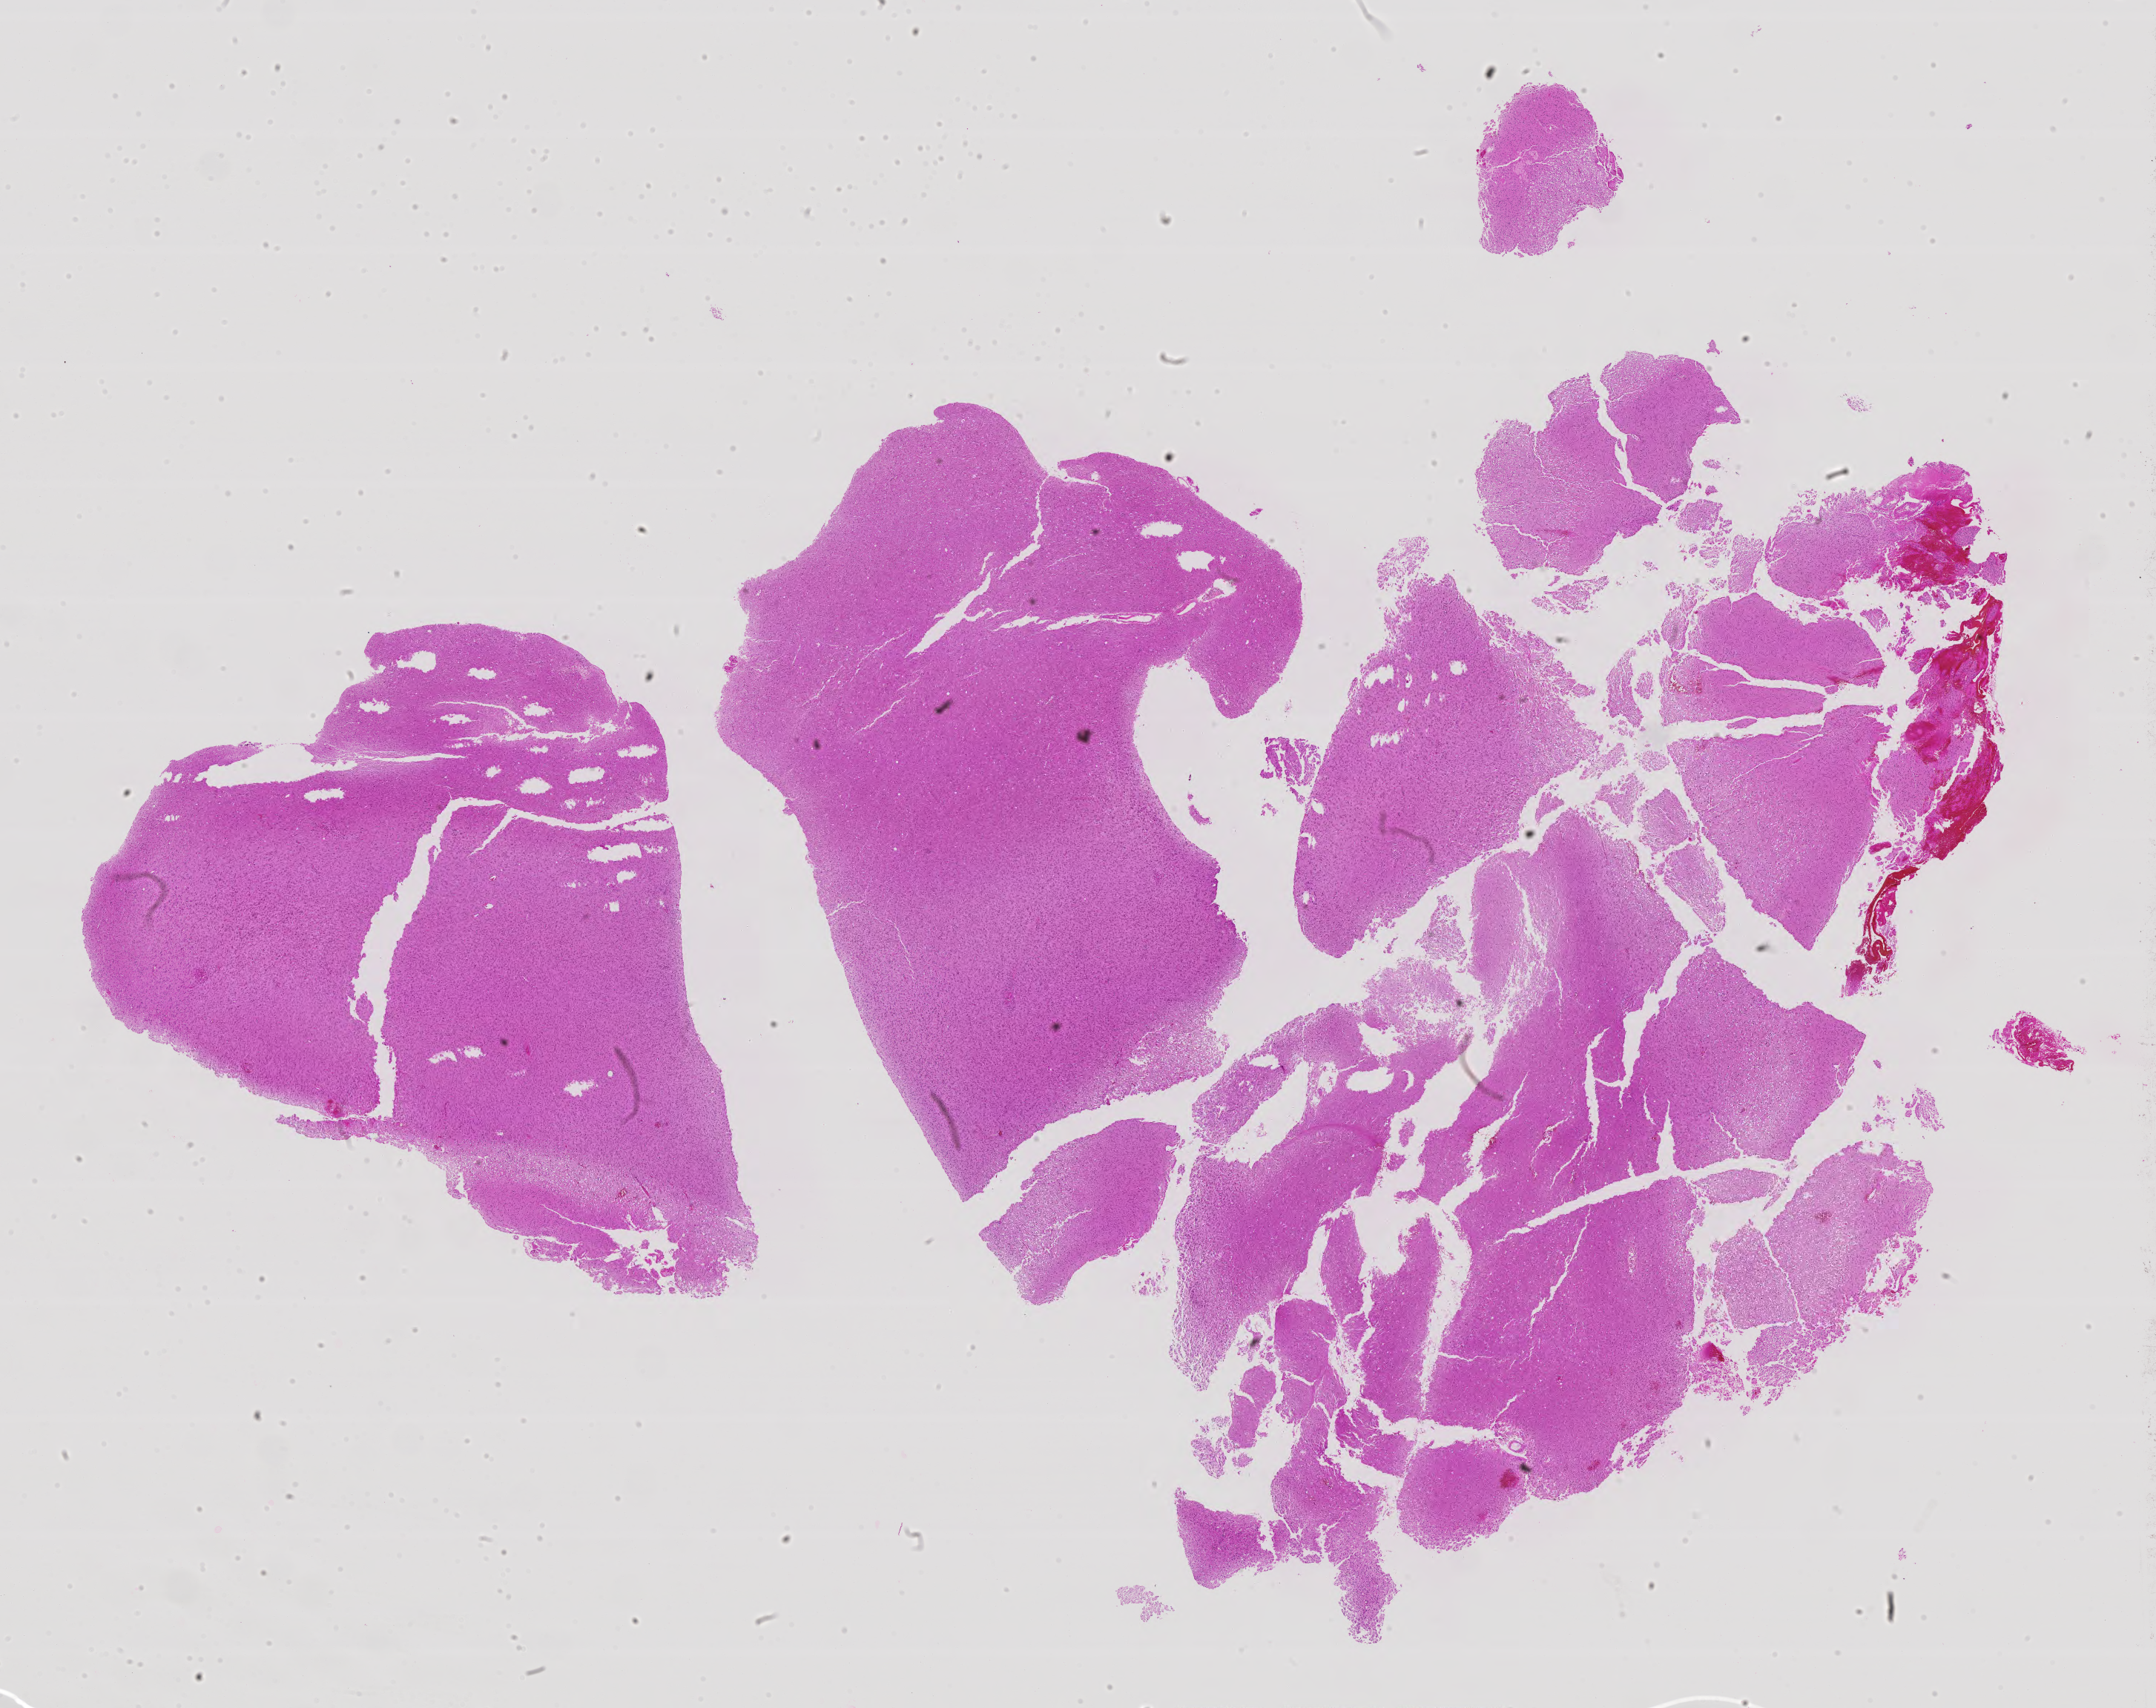
Digitized Hematoxylin and eosin (H&E) stained tissue section (whole slide), low-resolution overview of the scanned area, about 23.3 x 18.4 mm (from a 40x scan), formalin-fixed paraffin-embedded (FFPE) diagnostic section, sample: primary tumour, brain. Female patient; age at initial diagnosis 58 years. Histologic grade: G2 (moderately differentiated).
Diagnosis: Oligodendroglioma, NOS (cerebrum).